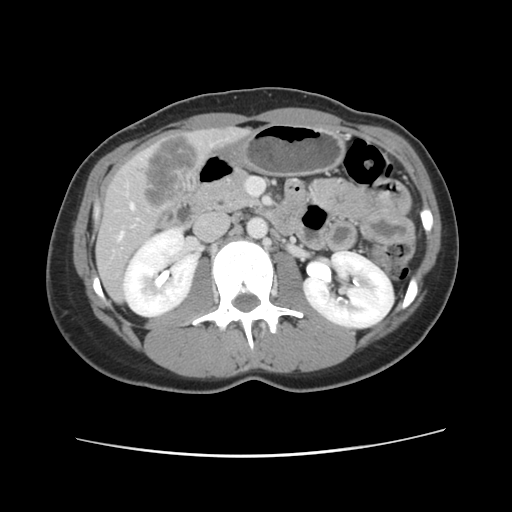
Contrast-enhanced abdominal CT, one axial slice. Slice 39 of 134 in the series (ordered by position). 120 kVp. Intravenous contrast given. Soft-tissue window (W 400 / L 40 HU). 2.5 mm slice thickness. 512 × 512 image matrix, field of view 339 × 339 mm. Female patient, age 33 years. Case-level facts recorded for this patient, not image findings: diagnosis: colorectal cancer liver metastases, imaged before liver resection; multiple liver metastases: yes; largest metastasis: 4.5 cm; disease in both lobes: yes.
Annotated regions visible in this slice (outlined manually by an expert reader):
- hepatic veins: bounding box <118,204,134,241> (left, top, right, bottom; pixels)
- liver: <96,128,246,300>
- planned liver remnant (the part of the liver to remain after resection): <96,241,128,301>
- liver metastasis: <143,134,200,210>